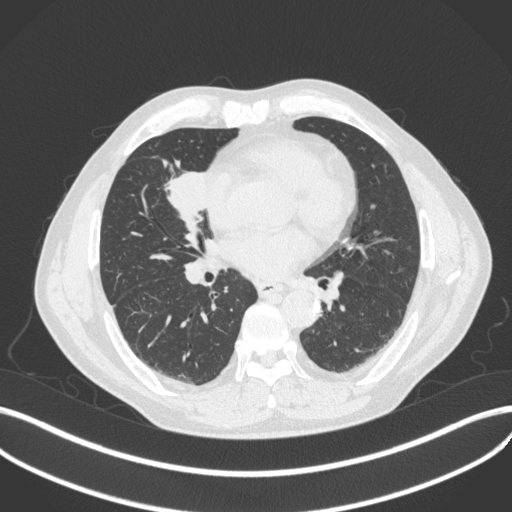
Chest CT, one axial slice; slice 189 of 429 in the series (ordered by position); lung window (W 1500 / L -600 HU); 1 mm slice thickness; 512 × 512 image matrix. Patient: male, 61 years. Case-level facts recorded for this patient, not image findings: clinical TNM (as recorded): T2b N1 M0.
Outlined on this slice (bounding box drawn by a radiologist):
- lung tumour (recorded histology: squamous cell carcinoma): bounding box <157,159,217,221> (left, top, right, bottom; pixels)